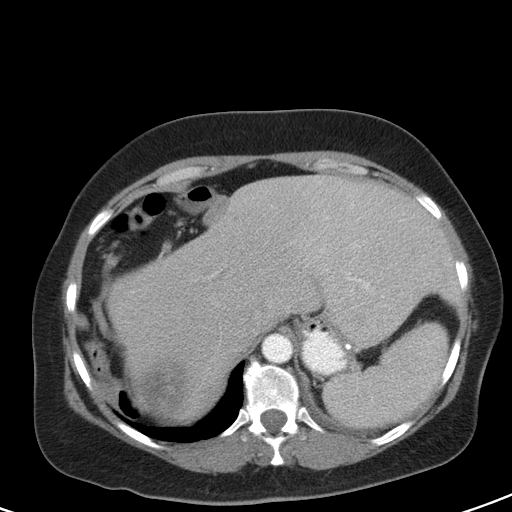
Contrast-enhanced abdominal CT, one axial slice; 120 kVp; intravenous contrast given; soft-tissue window (W 400 / L 40 HU); 5 mm slice thickness; 512 × 512 image matrix, field of view 356 × 356 mm. Female patient, age 51 years. From the clinical record (not read from this slice): diagnosis: adrenocortical carcinoma; tumour side: right adrenal; tumour size at pathology: 17 cm; Ki-67 index: 12 %; stage (as recorded): 2.
Annotated regions visible in this slice (semi-automatically segmented with operator editing):
- mass: bounding box <143,359,182,409> (left, top, right, bottom; pixels)